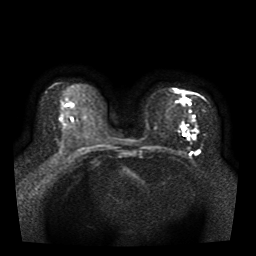
Breast MRI, one axial slice. Slice 21 of 41 in the series (ordered by position). Diffusion-weighted series; image 2 of 4 stored at this slice position (different b-values; order by instance number). 1.5 T. 5 mm slice thickness. 256 × 256 image matrix, field of view 330 × 330 mm. Female patient.
Annotated regions visible in this slice (outlined manually by an expert reader):
- tumour on diffusion-weighted imaging: bounding box <181,98,201,155> (left, top, right, bottom; pixels)